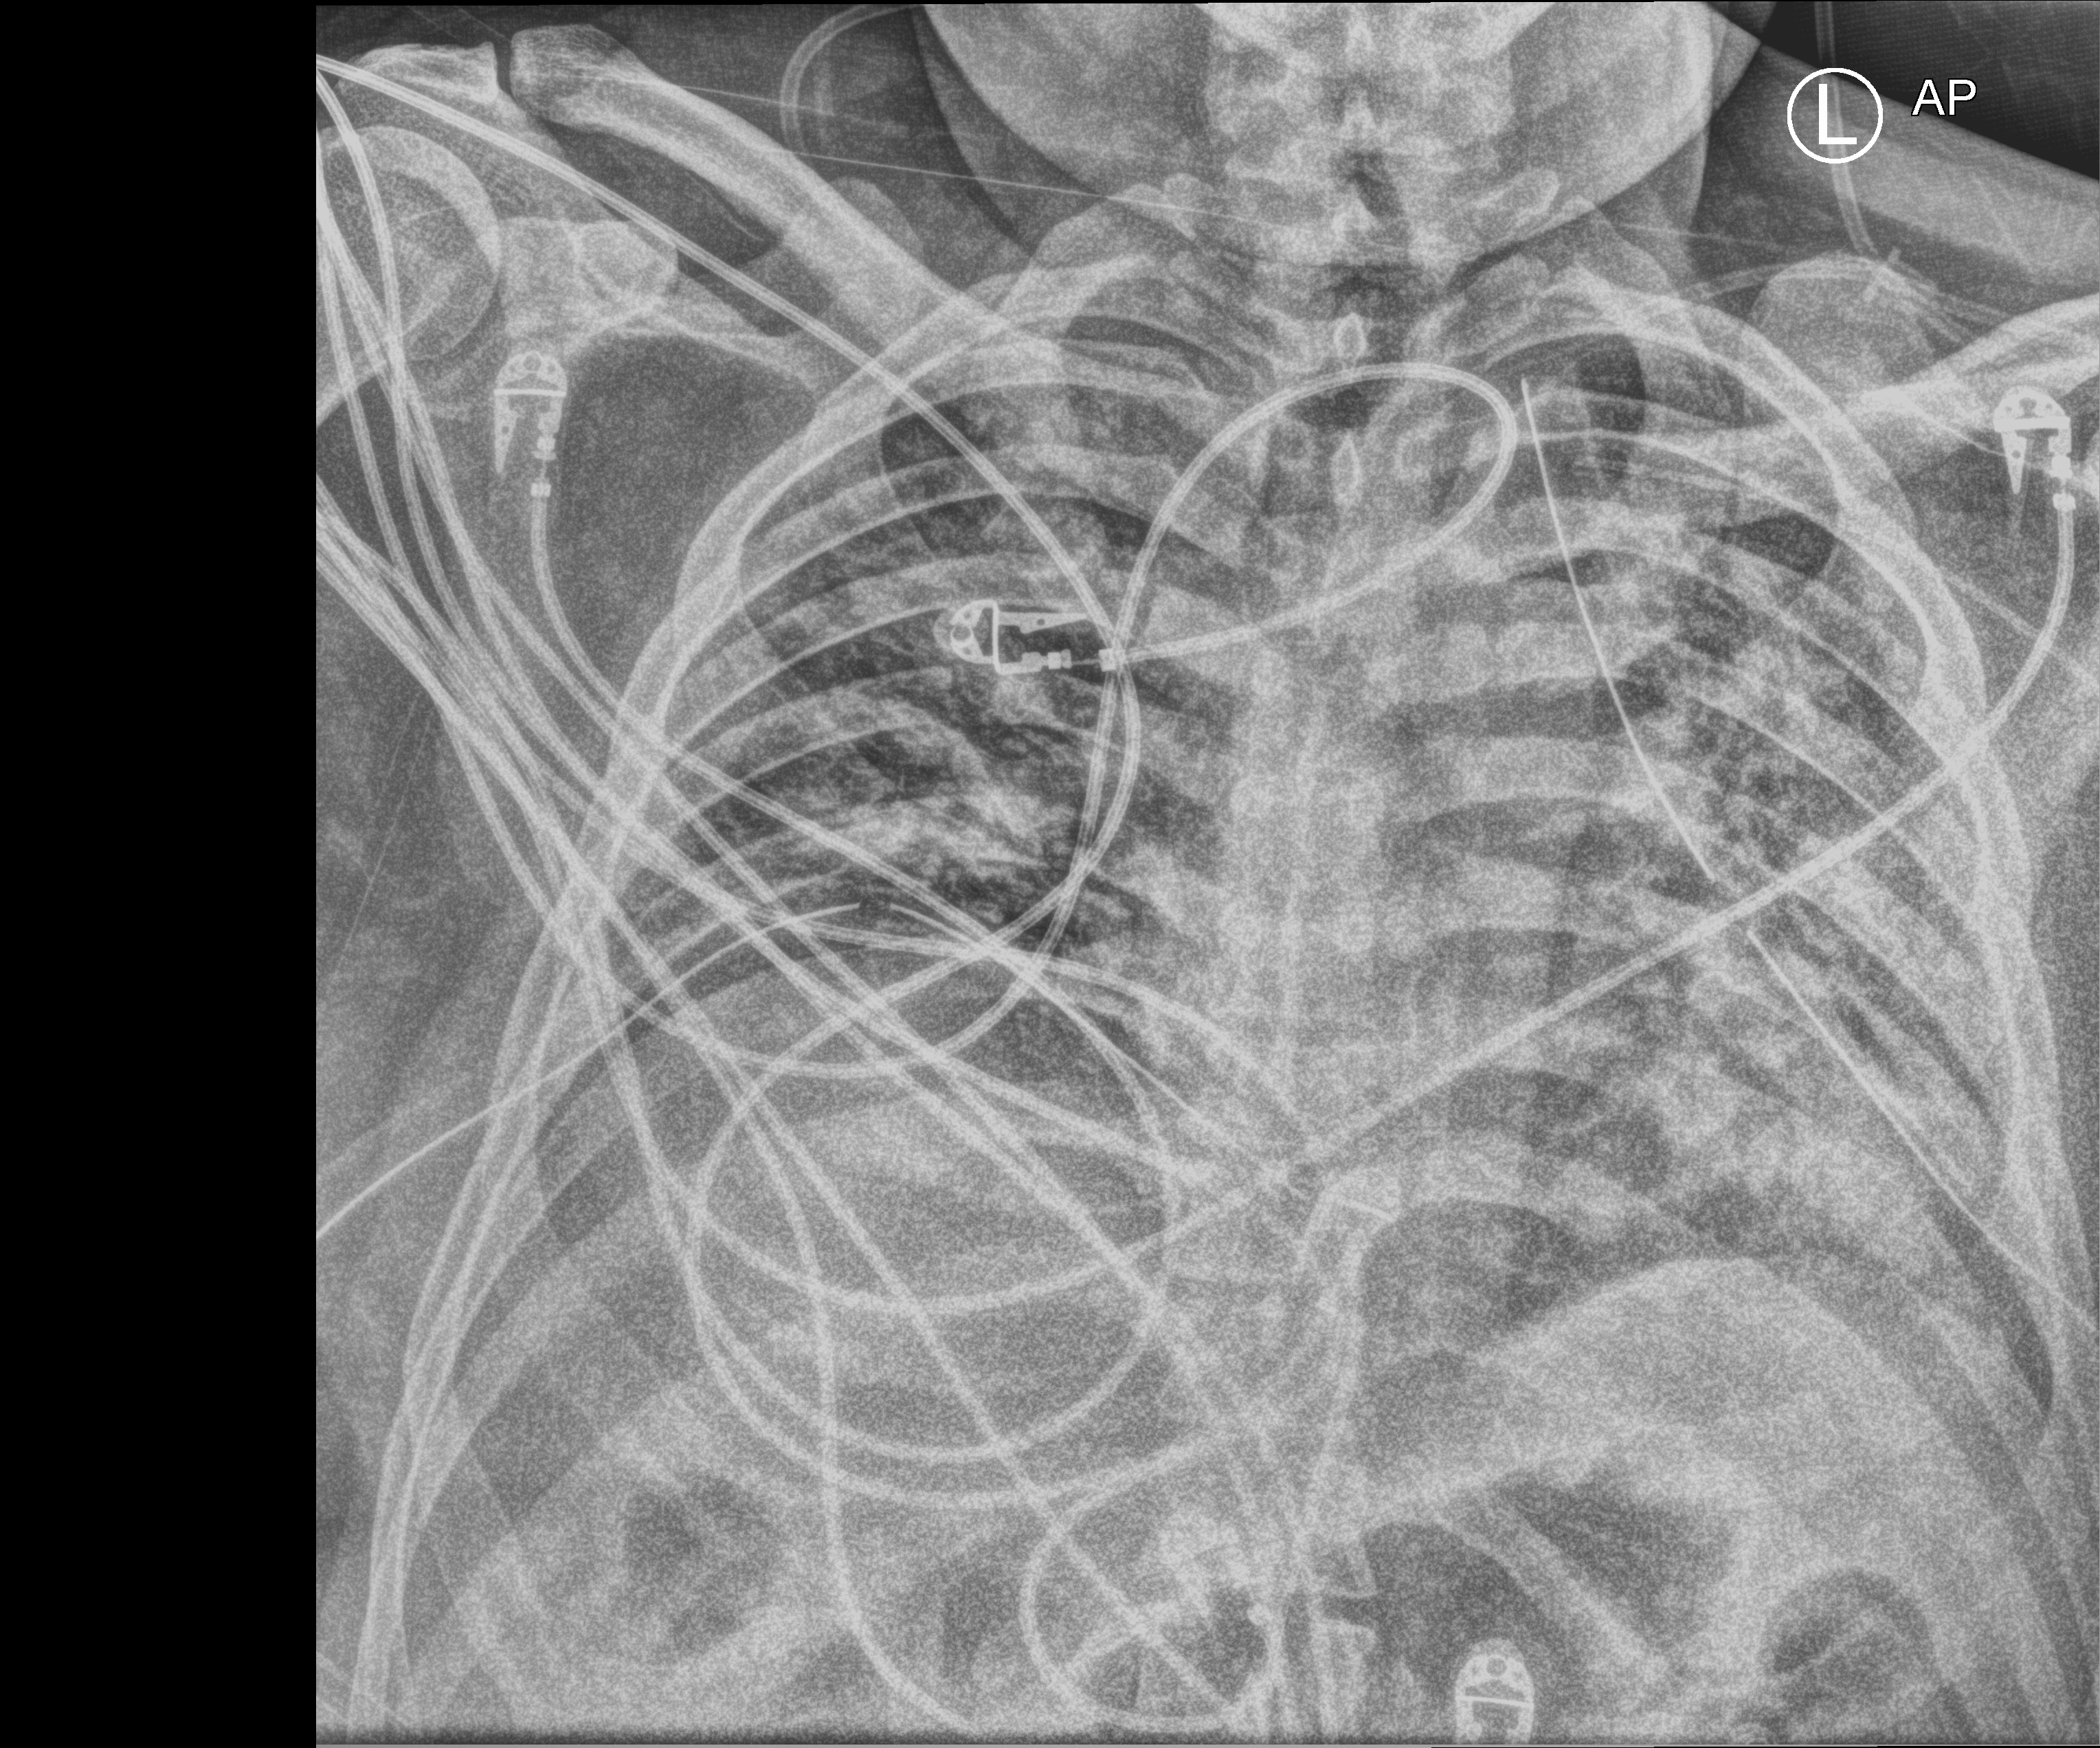
Chest X-ray (portable); anteroposterior (AP) projection. Patient hospitalised with COVID-19; male, aged 18–59 years.
Hospital-stay facts (about this admission, not read from this image; timing relative to this image not recorded): mechanically ventilated during this hospital stay: yes.